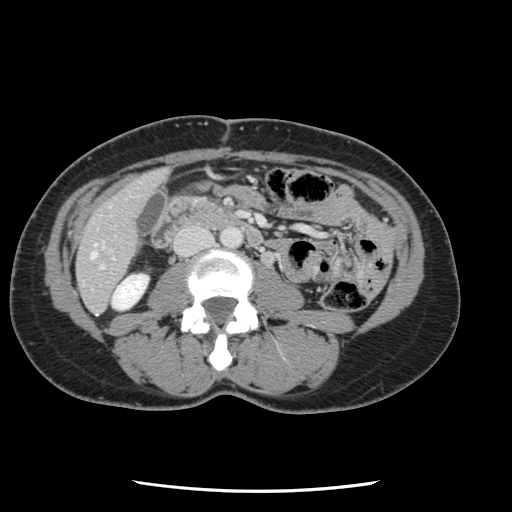
Contrast-enhanced abdominal CT, one axial slice; position 21 of 134 along the scan axis; 120 kVp; soft-tissue window (W 400 / L 40 HU); 512 × 512 image matrix, field of view 330 × 330 mm. Female patient, age 43 years. From the clinical record (not read from this slice): diagnosis: colorectal cancer liver metastases, imaged before liver resection; multiple liver metastases: yes; largest metastasis: 3.4 cm.
Annotated regions visible in this slice (manually delineated by an expert):
- hepatic veins: bounding box (x1, y1, x2, y2) in pixels: (91, 245, 96, 258)
- liver: (78, 170, 168, 312)
- planned liver remnant (the part of the liver to remain after resection): (77, 170, 167, 312)